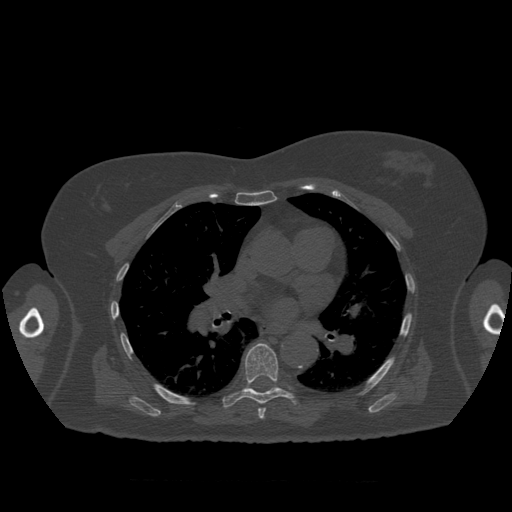
CT including the spine, one axial slice. Position 397 of 399 along the scan axis. Reconstruction kernel STANDARD. Bone window (W 1800 / L 400 HU). 1.25 mm slice thickness. 512 × 512 image matrix, field of view 404 × 404 mm. Patient age 81 years. Case-level facts recorded for this patient, not image findings: primary cancer: renal.
Structures marked on this image (semi-automatic segmentation, software-assisted and operator-edited):
- T7 vertebra: bounding box <223,343,297,420> (left, top, right, bottom; pixels)